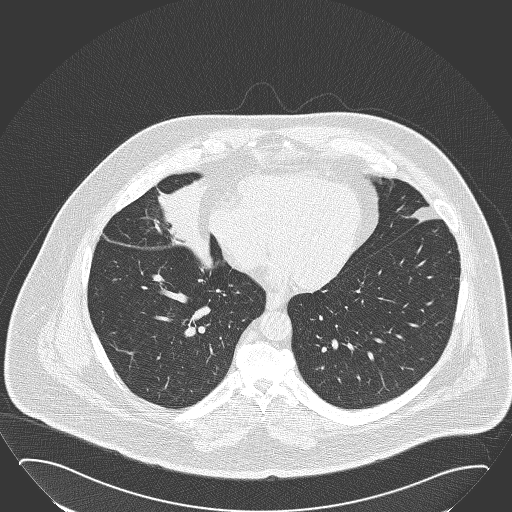
Chest CT (low-dose screening protocol), one axial image. Baseline annual screen. Lung window (W 1500 / L -600 HU). Lung (sharp) reconstruction kernel (B50f). Slice 106 of 168 in the series. 512 × 512 image matrix. Male participant, aged 61 years at enrolment. Former smoker at enrolment.
- Expert-annotated lung lesion, bounding box [x1, y1, x2, y2] px = [131, 167, 226, 257].
- The screening reader recorded 2 non-calcified nodules or masses ≥4 mm on this exam (right middle lobe, left lower lobe); which of them this box marks is not recorded.
- Official screen result: positive, change unspecified: nodule(s) >= 4 mm or enlarging nodule(s), mass(es), or other non-specific abnormalities suspicious for lung cancer.
- Later outcome: lung cancer diagnosed 47 days after this screen — basaloid squamous cell carcinoma, right middle lobe, right hilum, poorly differentiated (G3), stage IIB (AJCC 6th edition), 95 mm at pathology.